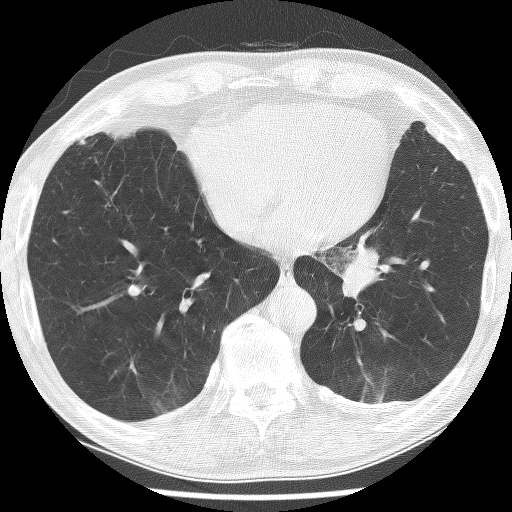
Low-dose screening chest CT, axial slice; first (baseline) screen; lung window (W 1500 / L -600 HU); 2.5 mm slice thickness; 120 kVp. Male participant, aged 74 years at enrolment. Current smoker at enrolment.
- Expert reader's lesion annotation, bounding box [x1, y1, x2, y2] px = [318, 228, 425, 321].
- Screening reader's record for this exam (one nodule recorded; not confirmed to be the boxed lesion): non-calcified nodule or mass ≥4 mm, left lower lobe, 30 × 27 mm, spiculated (stellate) margins, soft tissue attenuation.
- Official screen result: positive, change unspecified: nodule(s) >= 4 mm or enlarging nodule(s), mass(es), or other non-specific abnormalities suspicious for lung cancer.
- Participant outcome: lung cancer diagnosed 151 days after this screen — adenocarcinoma, NOS, left lower lobe, stage IIIA (AJCC 6th edition), 49 mm at pathology.